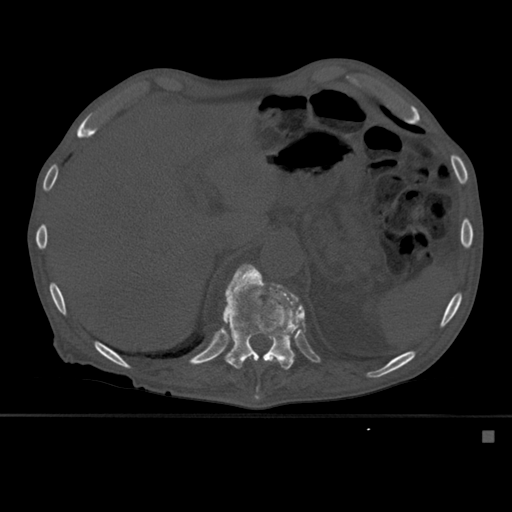
CT including the spine, one axial slice; bone window (W 1800 / L 400 HU); 1.5 mm slice thickness; 512 × 512 image matrix. Male patient, age 78 years. Case-level facts recorded for this patient, not image findings: primary cancer: prostate.
Structures marked on this image (semi-automatically segmented with operator editing):
- T11 vertebra: bounding box [x1, y1, x2, y2] px = [222, 263, 294, 400]
- T12 vertebra: [222, 271, 306, 362]